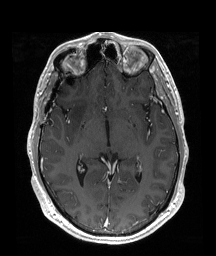
Brain MRI from a brain-tumour surgery series, one axial slice; position 108 of 192 along the scan axis; T1-weighted post-contrast; 216 × 256 image matrix. From the clinical record (not read from this slice): histopathology: Astrocytoma; WHO grade: 2; IDH mutation: yes.
Structures marked on this image (expert manual segmentation):
- tumour: bounding box [x1, y1, x2, y2] px = [71, 94, 90, 132]